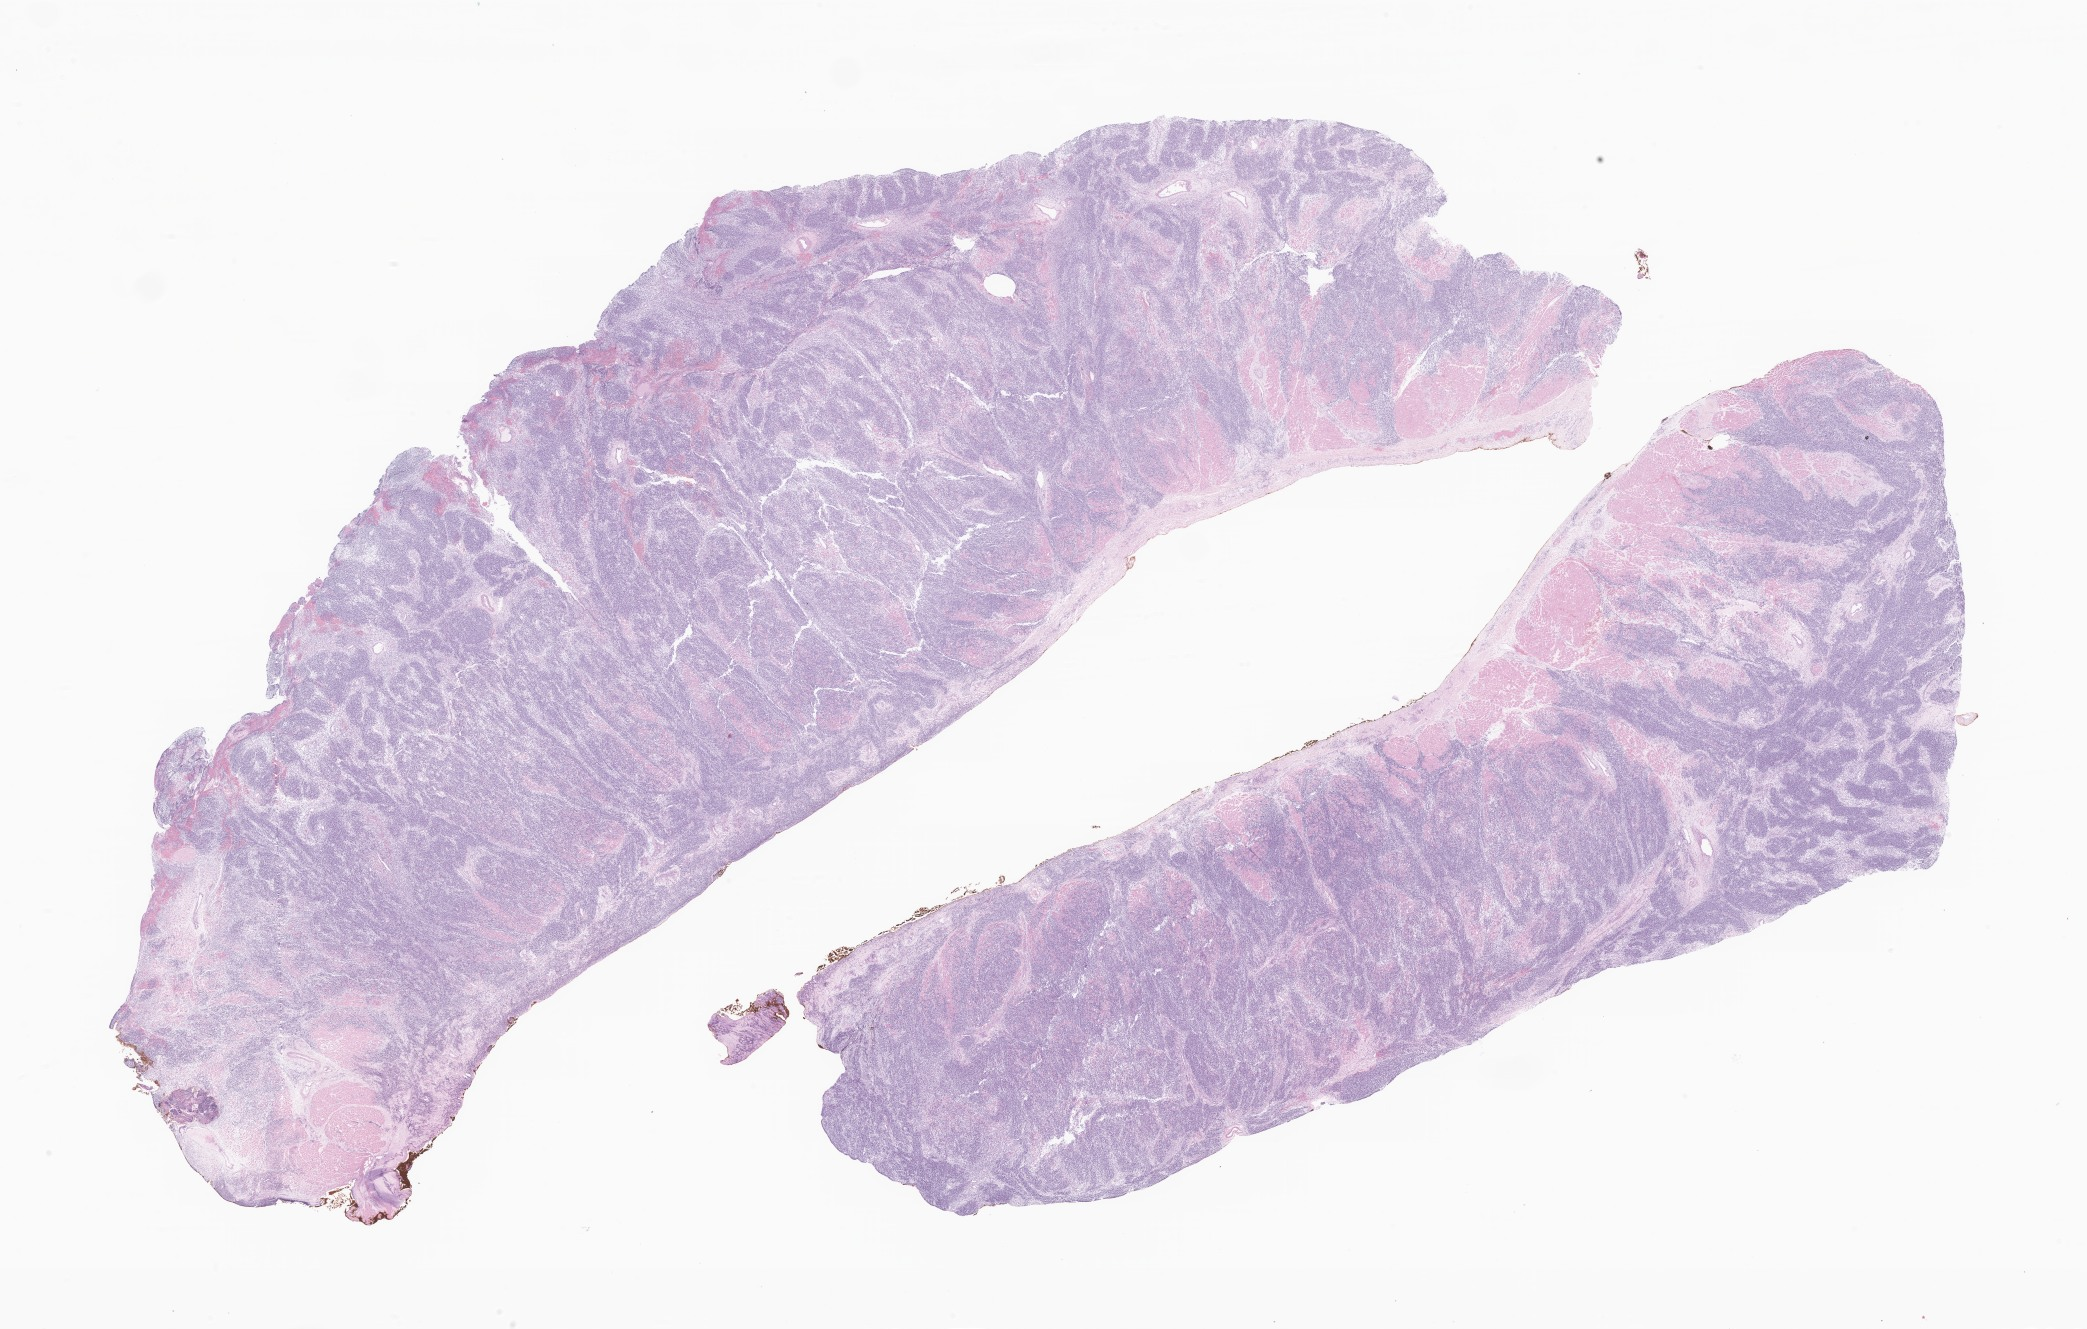
Whole-slide image, H&E stain of tumor tissue from the abdomen — a low-resolution overview of the entire scanned area, about 35.2 x 22.4 mm; FFPE section. Patient: female, age 54 months (4 years 6 months).
Diagnosis: Rhabdomyosarcoma, NOS.